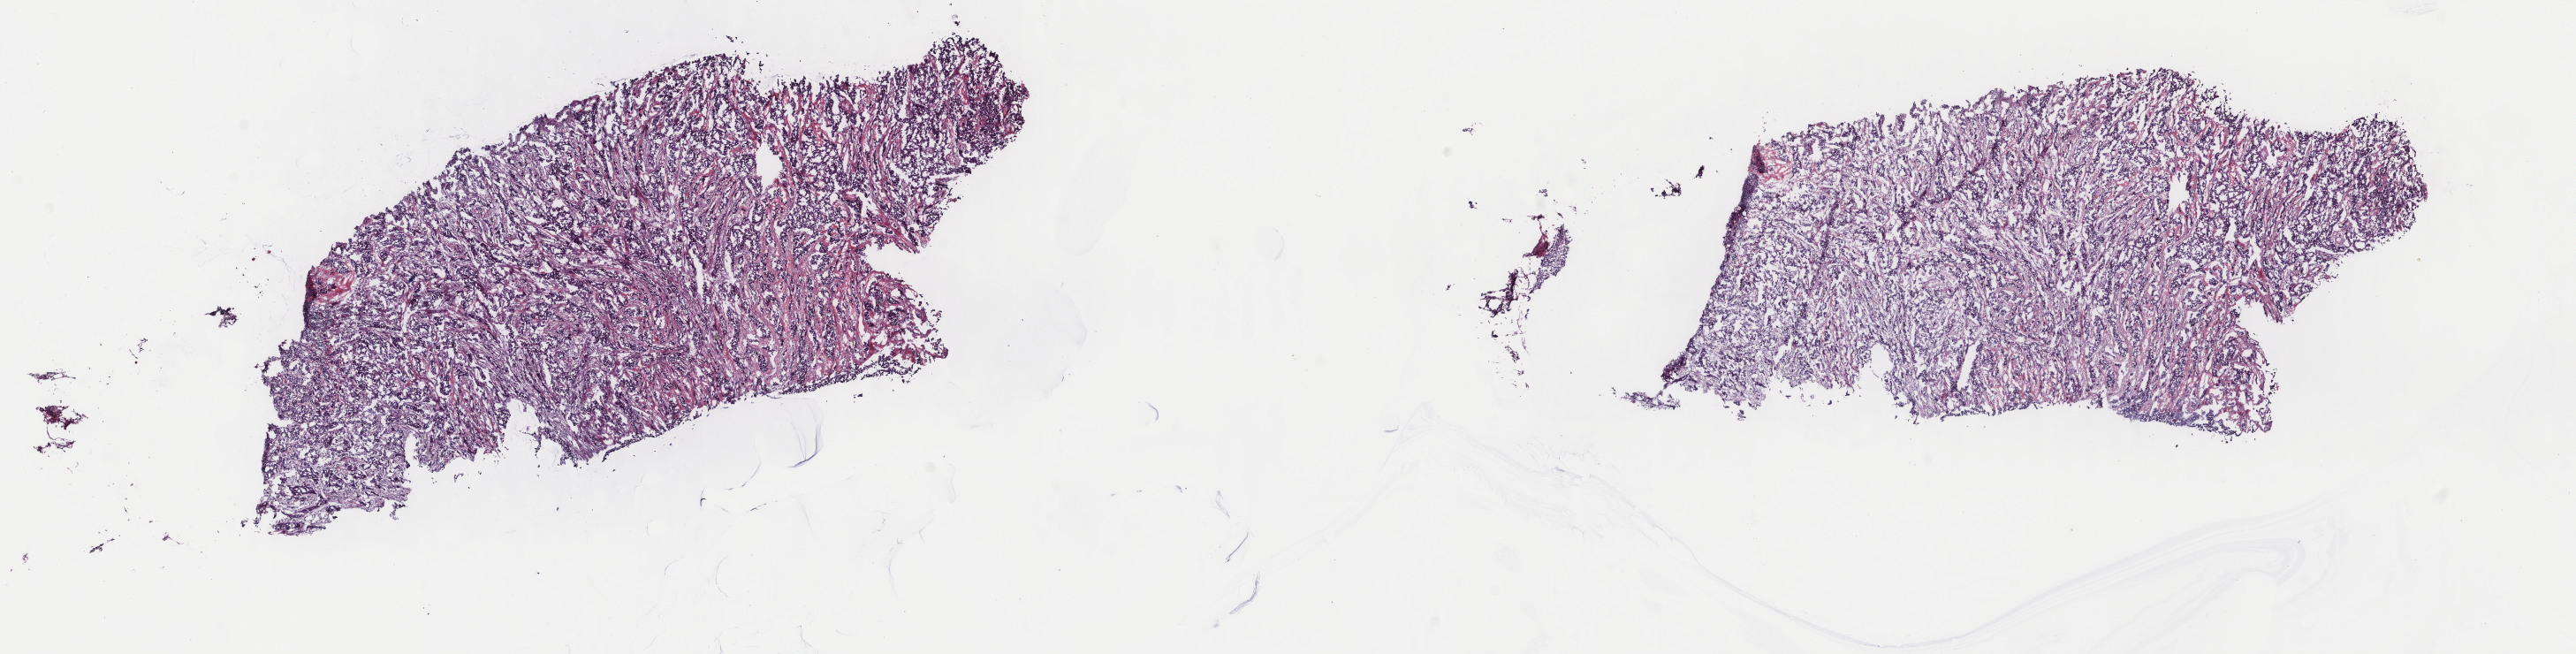
Hematoxylin and eosin (H&E) stained whole-slide image — low-resolution overview of the scanned area, about 23.1 x 5.9 mm (acquisition: 40x scan); frozen section from the top of the tissue portion; primary tumour sample from the breast. Patient: male, age at initial diagnosis 51 years. Composition of this section per pathologist review: tumour cells 80%, tumour nuclei 80%, normal cells 0%, stromal cells 20%, necrosis 0%. Infiltration values recorded for this section: lymphocyte infiltration 0%, monocyte infiltration 0%, neutrophil infiltration 0%.
- lymph nodes positive (case pathology): 0 of 14 examined
- AJCC pathologic stage: IIA (7th edition)
- histologic diagnosis: Infiltrating duct carcinoma, NOS